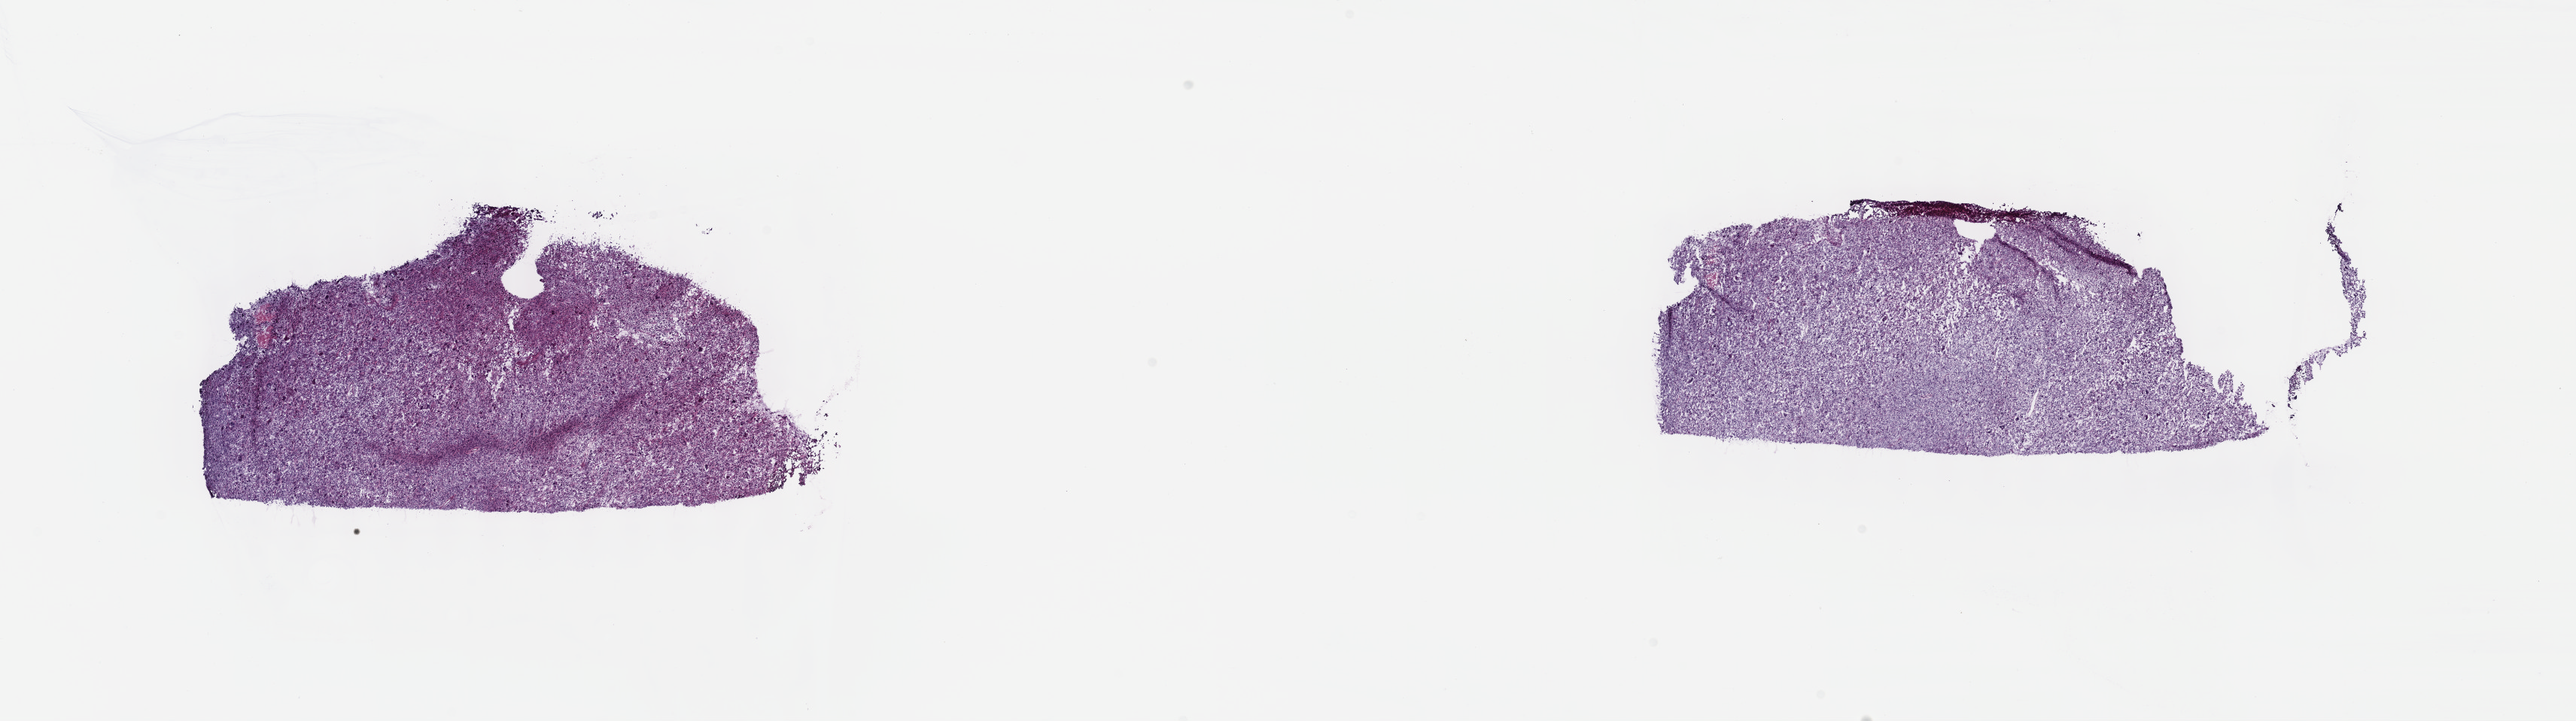
Whole-slide histology image, Hematoxylin and eosin (H&E) stained, low-resolution overview of the scanned area, about 27.7 x 7.7 mm (from a 40x scan), frozen section from the top of the tissue portion, sample: primary tumour, connective, subcutaneous and other soft tissues. Patient: male, age at initial diagnosis 60 years. Slide review estimates, as recorded: tumour cells 100%, tumour nuclei 80%, normal cells 0%, stromal cells 0%, necrosis 0%. Inflammatory infiltration, as recorded: lymphocyte infiltration 2%, monocyte infiltration 0%, neutrophil infiltration 0%.
Pathologic diagnosis: Undifferentiated sarcoma (connective, subcutaneous and other soft tissues of lower limb and hip).